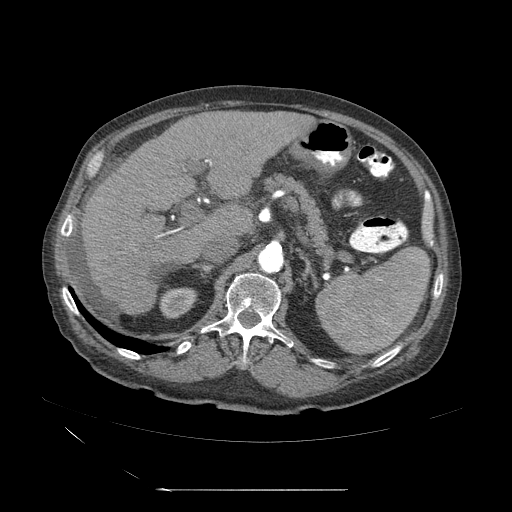
Contrast-enhanced abdominal CT (liver protocol), one axial slice; position 27 of 71 along the scan axis; reconstruction kernel STANDARD; 120 kVp; soft-tissue window (W 400 / L 40 HU); 512 × 512 image matrix, field of view 440 × 440 mm. Case-level facts recorded for this patient, not image findings: diagnosis: hepatocellular carcinoma (patient treated with transarterial chemoembolisation; whether this scan precedes or follows treatment is not stated here); TNM stage (as recorded): Stage-II; Child-Pugh class: A; tumour size: 1 cm.
Structures marked on this image (semi-automatic segmentation, software-assisted and operator-edited):
- abdominal aorta: box from (x=258, y=245) to (x=284, y=274) px
- liver parenchyma outside the tumour (the mass and vessels are separate outlines, so this box may not span the whole liver): (x=77, y=113)–(x=298, y=318)
- liver vessels: (x=138, y=161)–(x=239, y=264)